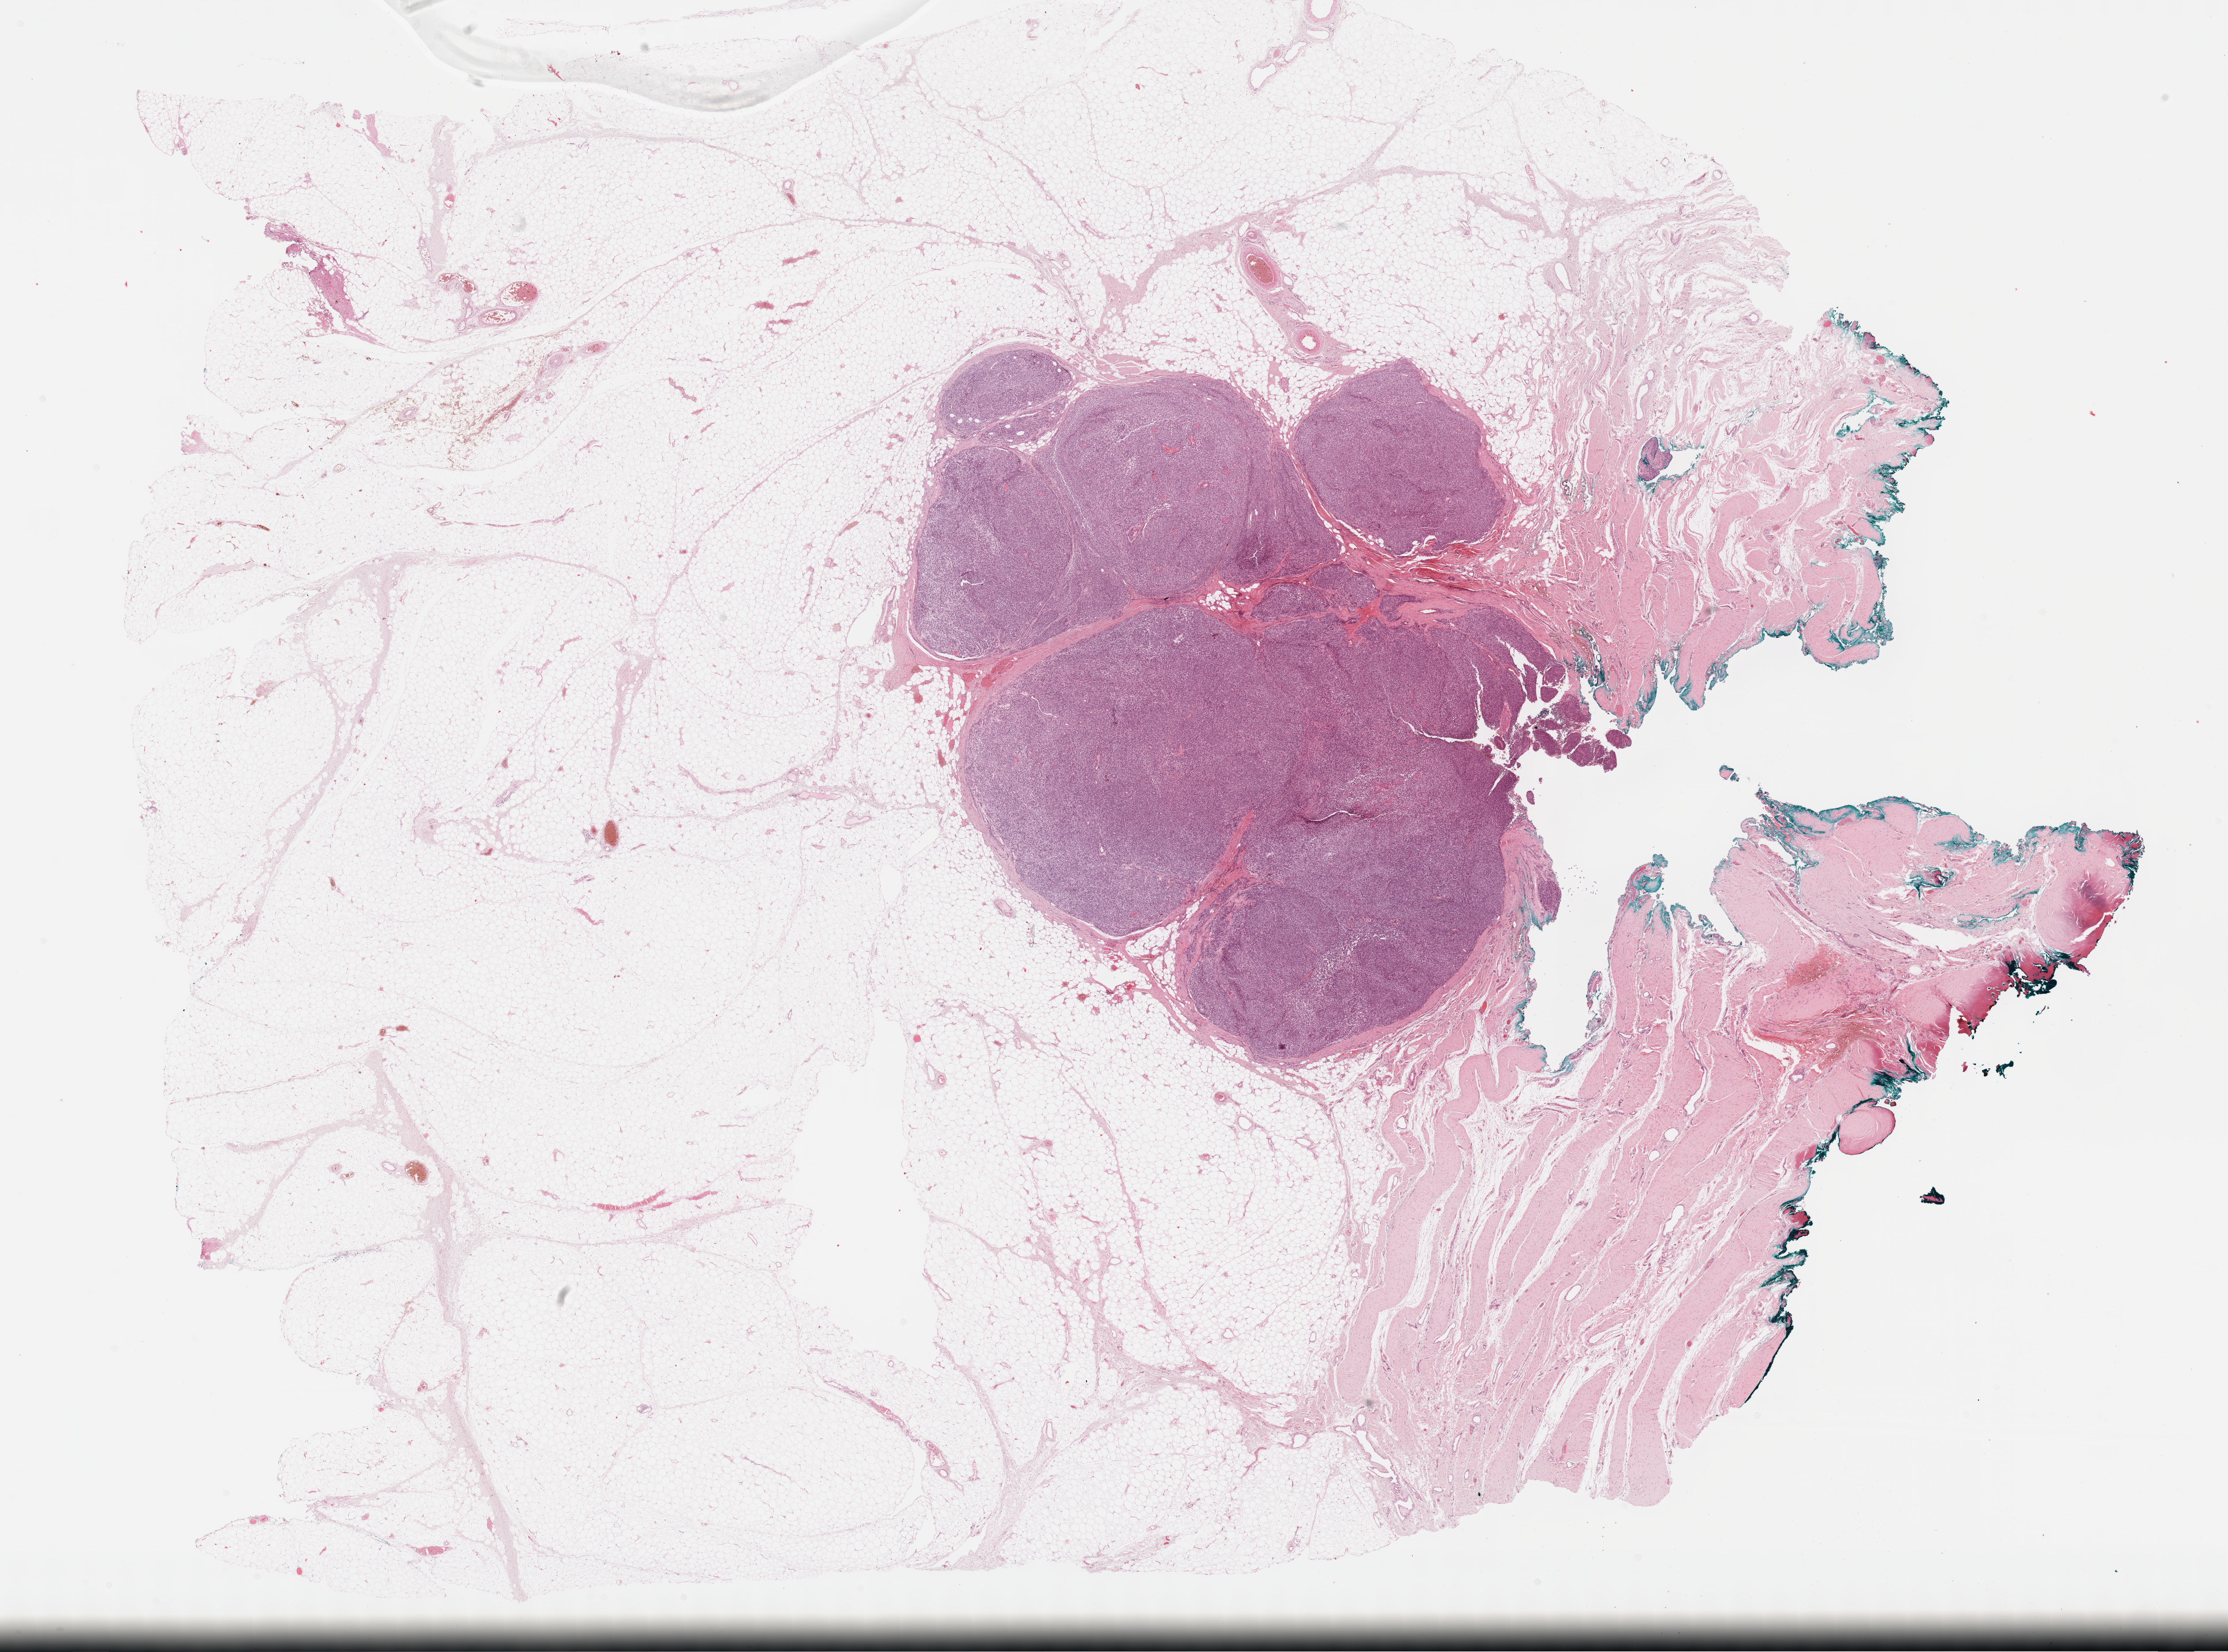
H&E whole-slide image — low-resolution overview of the scanned area, about 31.2 x 23.1 mm (from a 40x scan), formalin-fixed paraffin-embedded (FFPE) diagnostic section, metastatic tumour sample, sampled site: connective, subcutaneous and other soft tissues of thorax. Patient: male, age at initial diagnosis 70 years.
This section: metastatic tumour tissue. Patient diagnosis: Malignant melanoma, NOS.